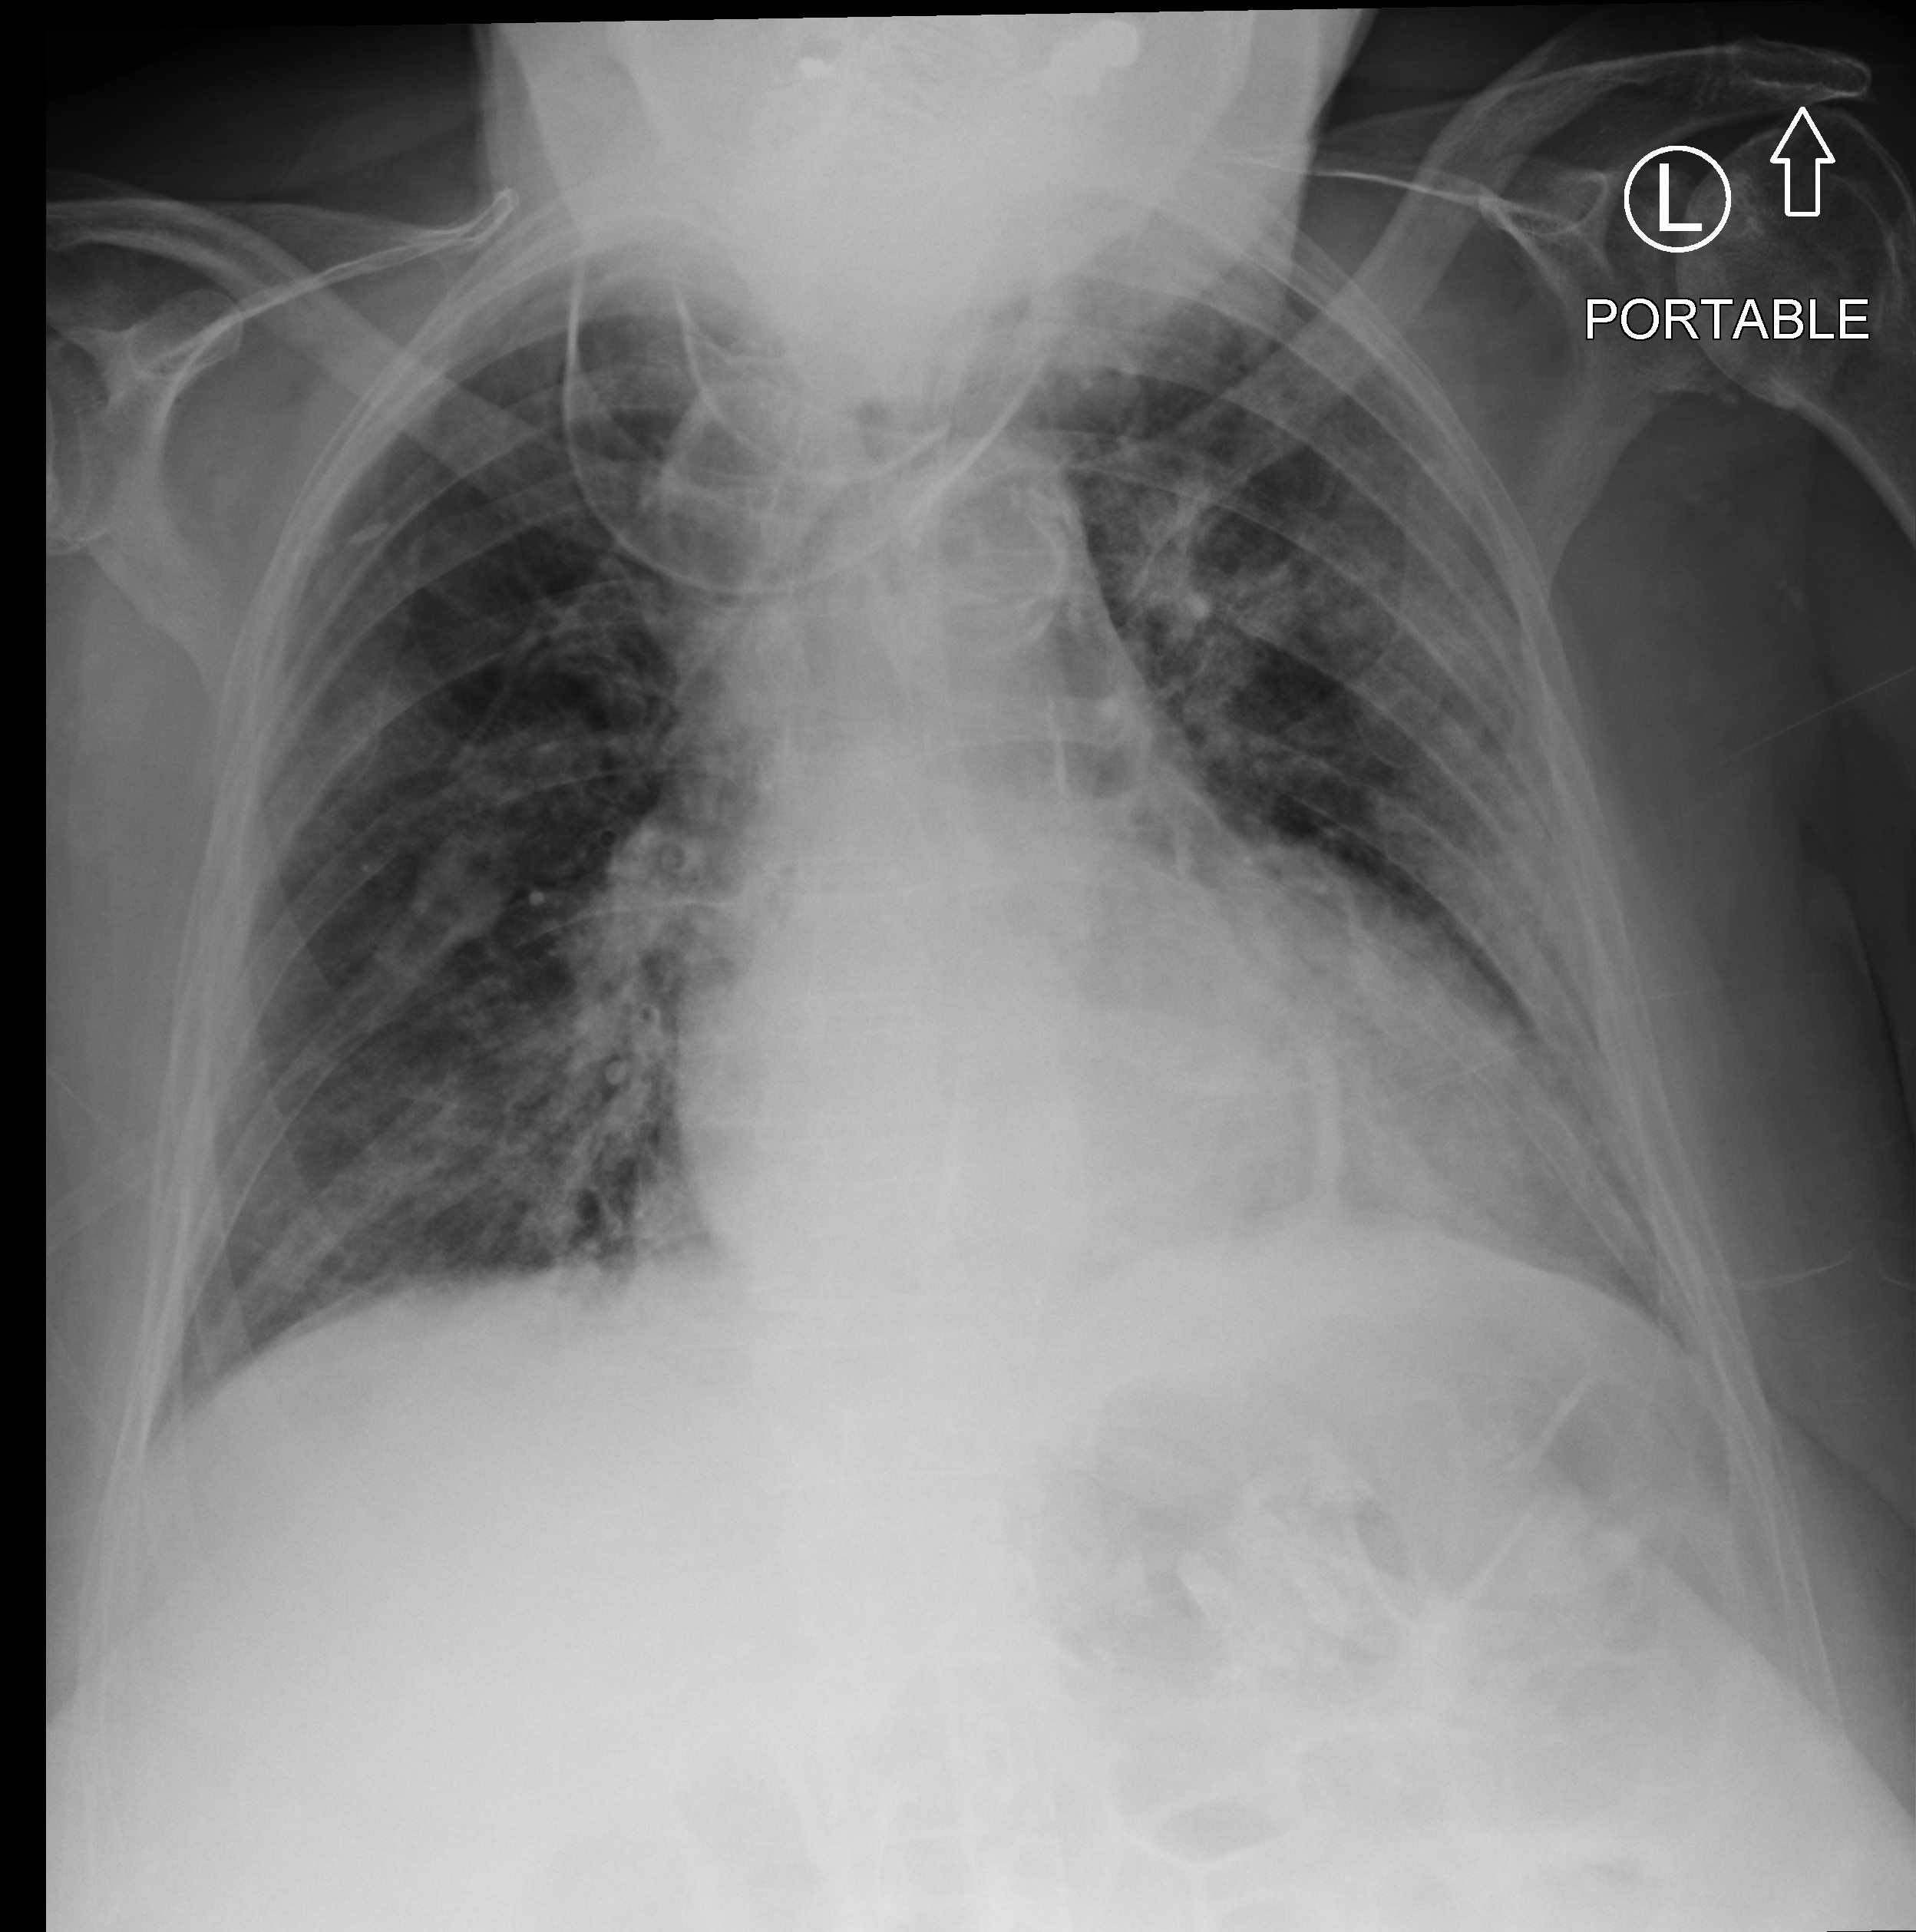
Bedside chest radiograph (computed radiography); anteroposterior (AP) projection. Female patient hospitalised with COVID-19, age 75–90 years.
Hospital-stay facts (about this admission, not read from this image; timing relative to this image not recorded): hypertension (admission record): yes; smoking status (admission record): never.